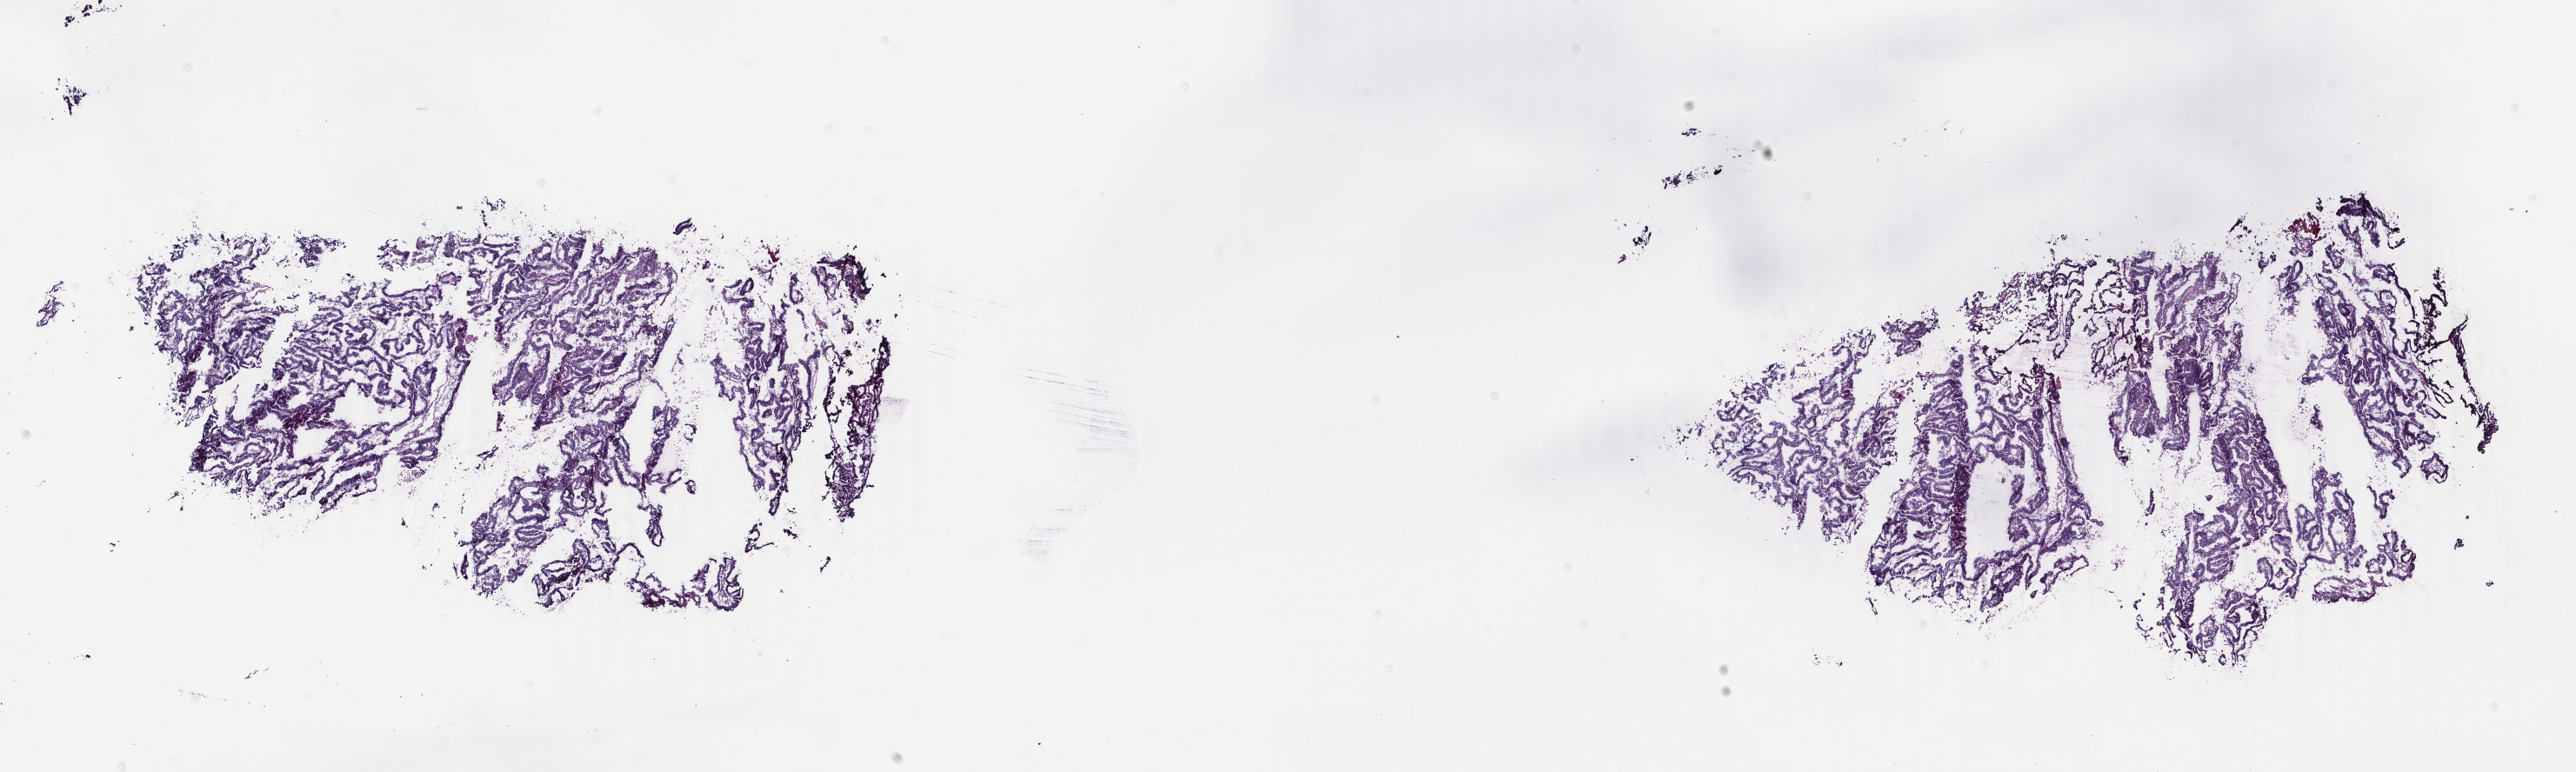
H&E-stained whole-slide image, whole scanned area (about 23.6 x 7.1 mm, acquisition: 40x scan) shown as a low-resolution overview; frozen section; uterus, primary tumour sample. Patient: female, age at initial diagnosis 69 years. Histologic grade: G1 (well differentiated). Slide review estimates, as recorded: tumour cells 100%, tumour nuclei 85%, normal cells 0%, stromal cells 0%, necrosis 0%. Inflammatory infiltration, as recorded: lymphocyte infiltration 0%, monocyte infiltration 0%, neutrophil infiltration 0%.
Histologic diagnosis: Endometrioid adenocarcinoma, NOS (endometrium). FIGO stage: IA.